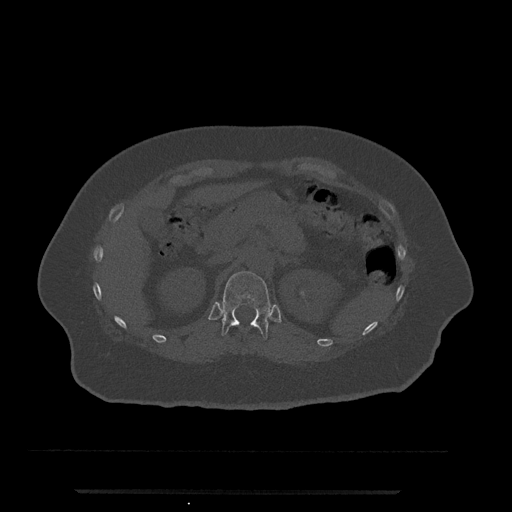
CT including the spine, one axial slice. Position 176 of 797 along the scan axis. Reconstruction kernel Br40s/3. Bone window (W 1800 / L 400 HU). 0.5 mm slice thickness. 512 × 512 image matrix, field of view 440 × 440 mm. Patient: female, 51 years. From the clinical record (not read from this slice): primary cancer: neuro.
Outlined on this slice (semi-automatically segmented with operator editing):
- T12 vertebra: bounding box (x1, y1, x2, y2) in pixels: (222, 271, 271, 340)